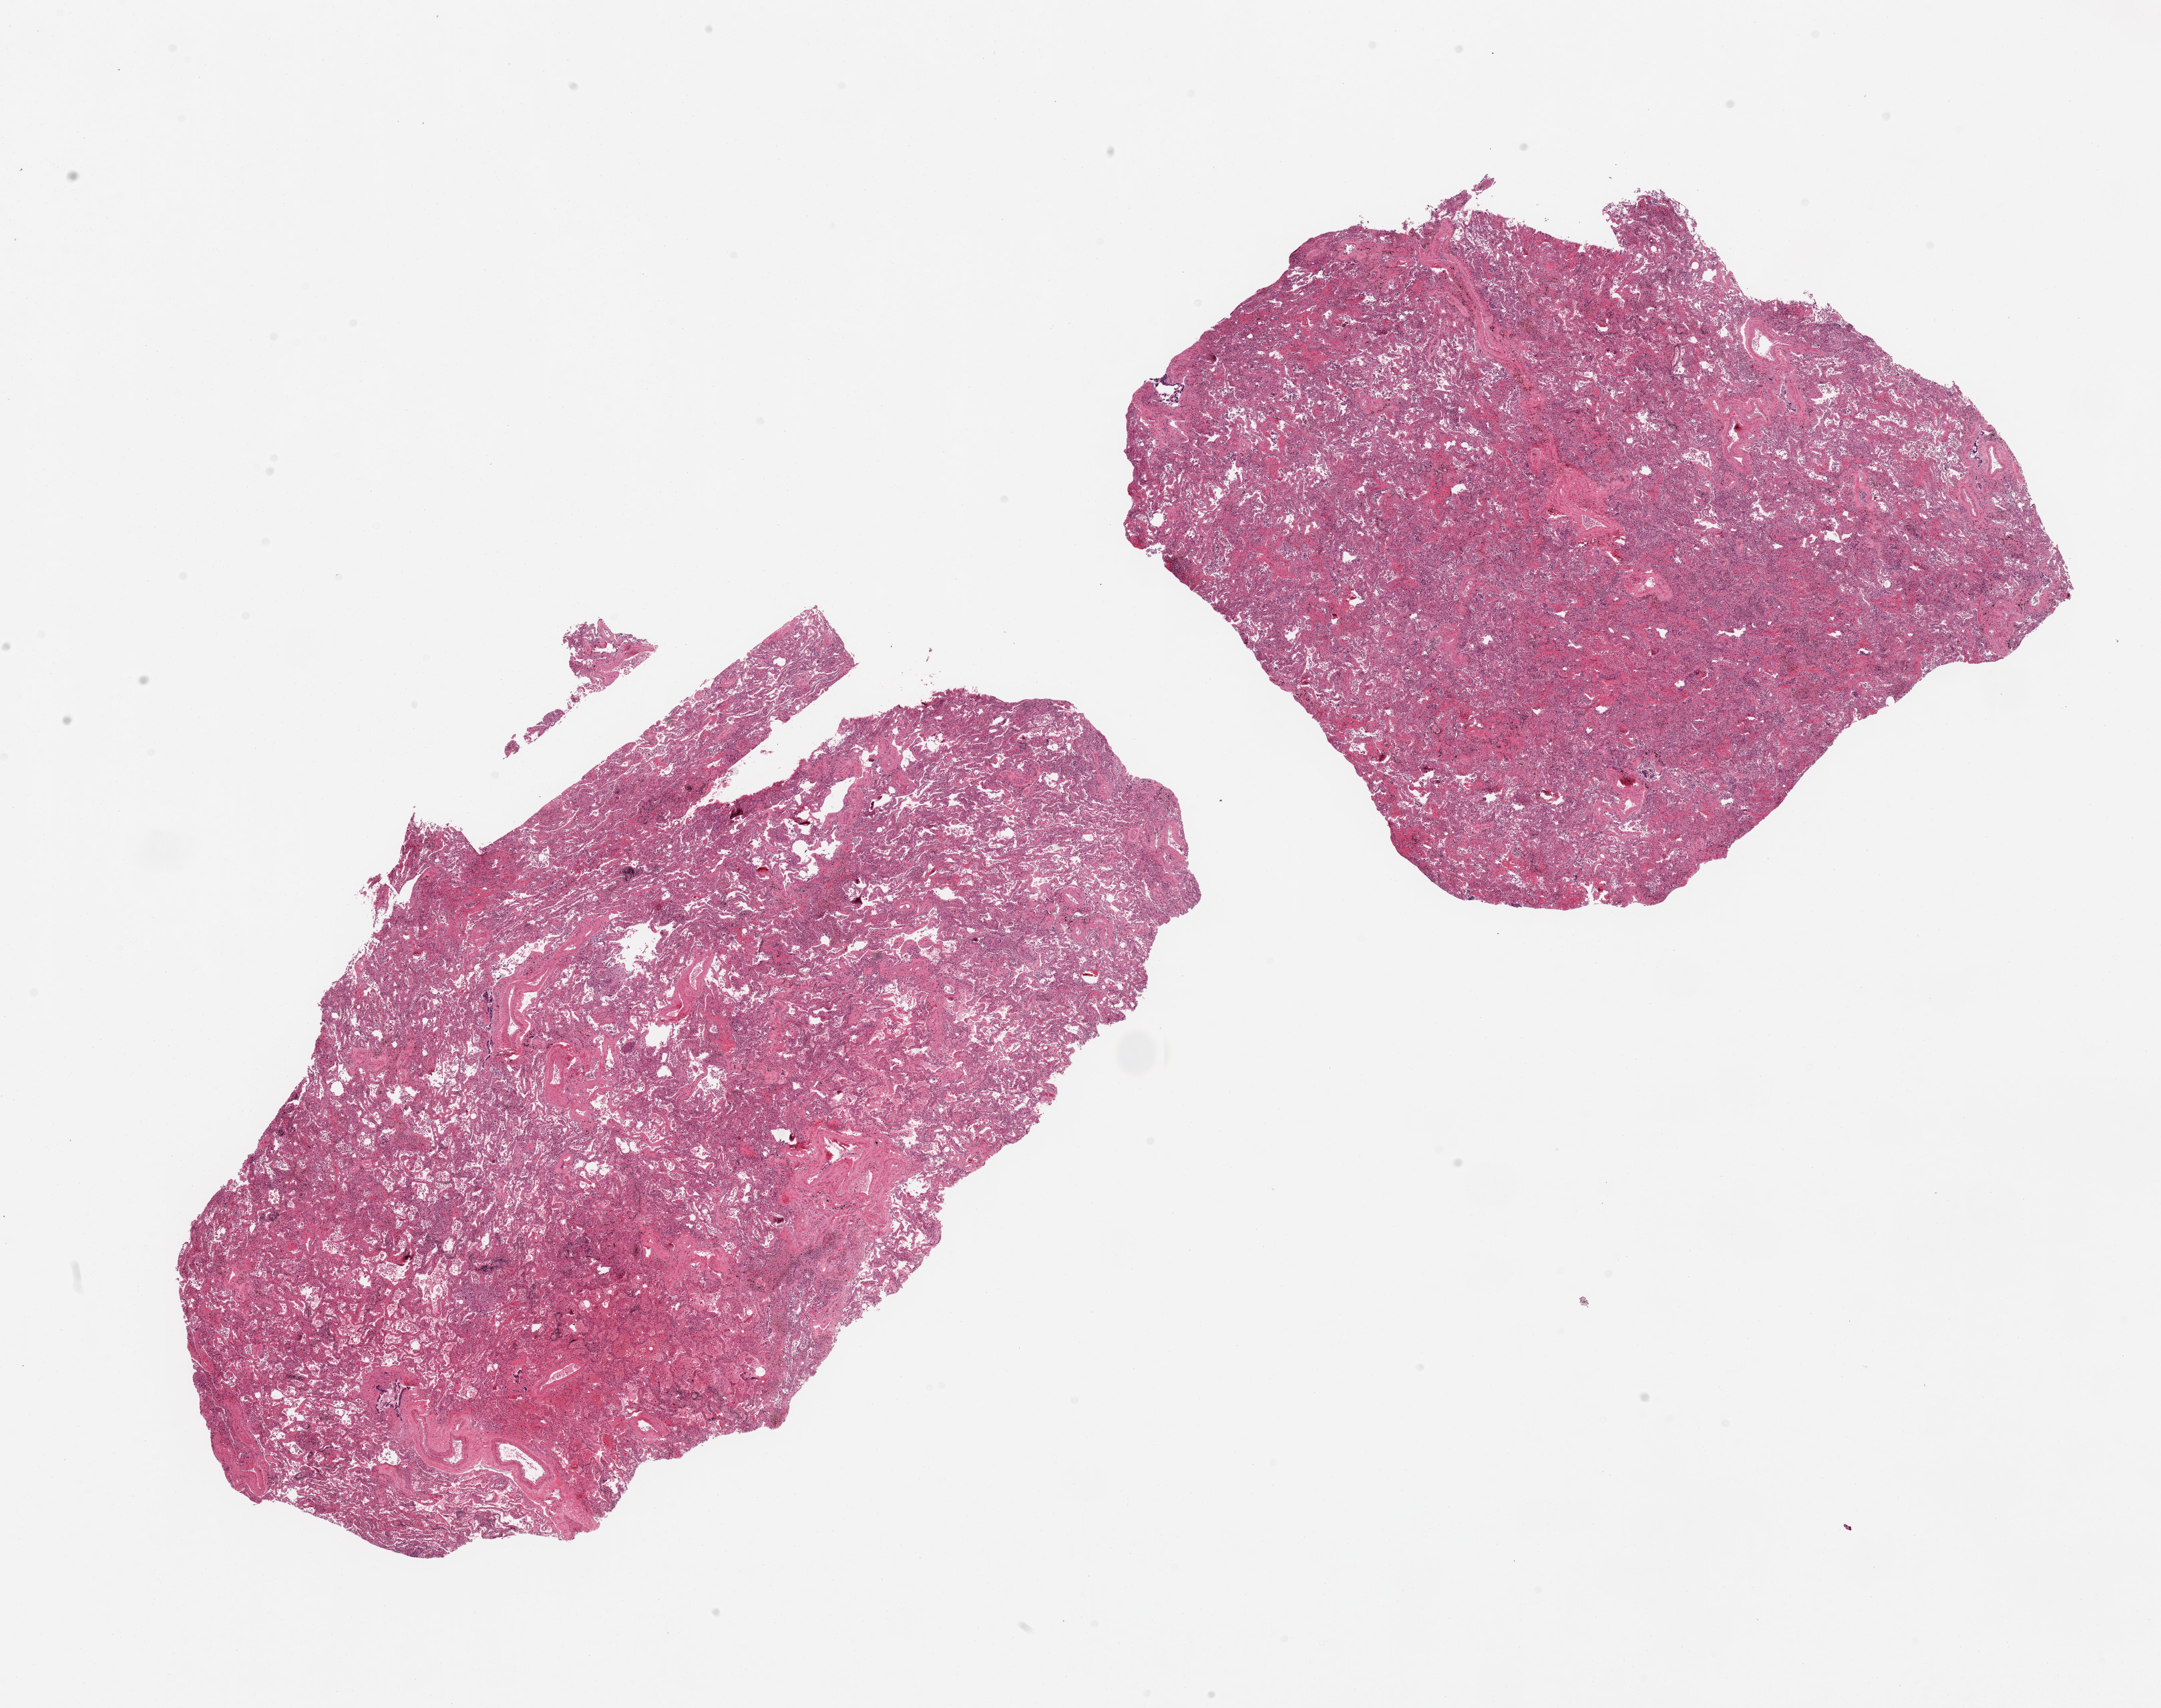
Digitized hematoxylin and eosin (H&E)-stained section, shown as a low-resolution overview of the whole scanned area (about 25.6 x 20.2 mm, acquisition: 20x scan), PAXgene-fixed paraffin-embedded (PFPE) section, sampled site (target tissue): lung, tissue donor sample. Male donor.
- reviewer comment on this tissue sample: 2 pieces, marked chronic congestion/fibrosing pneumonitis